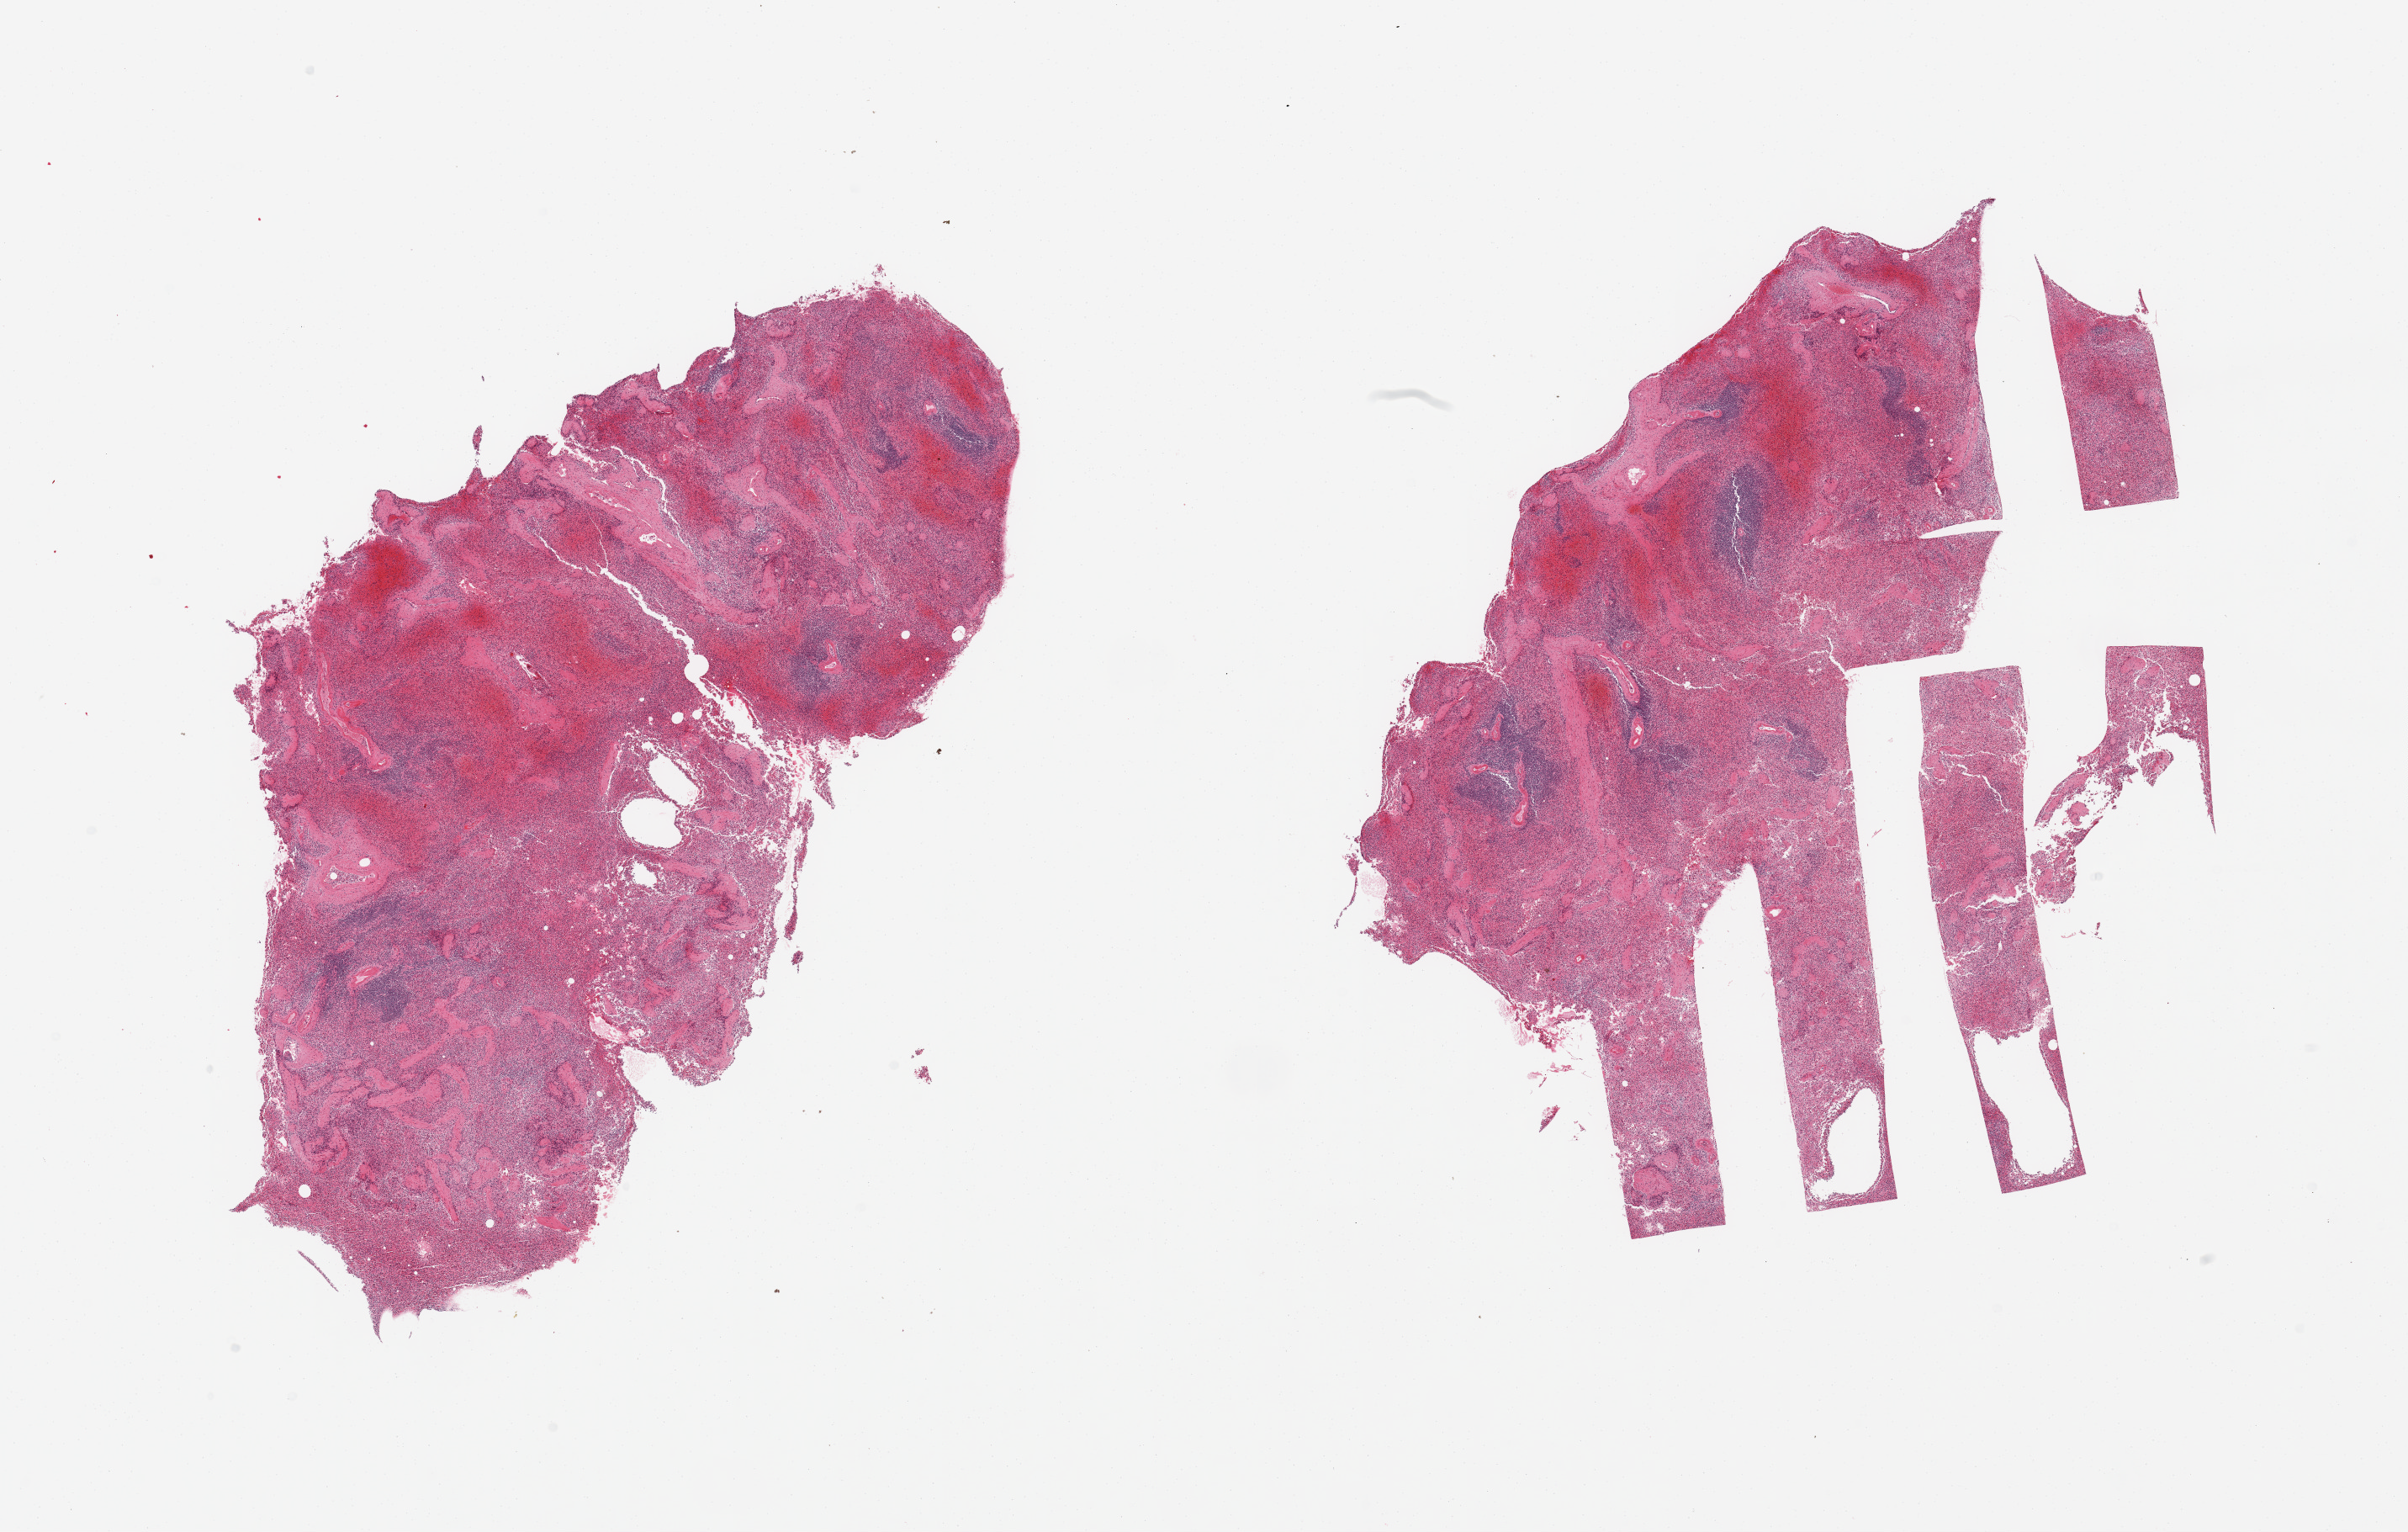
Digitized H&E-stained section — low-resolution overview of the scanned area, about 22.6 x 14.4 mm, PAXgene-fixed, paraffin-embedded tissue, target tissue: spleen, tissue donor sample. Donor: male.
Pathologist's review note for this sample: 2 pieces, moderate congestion.